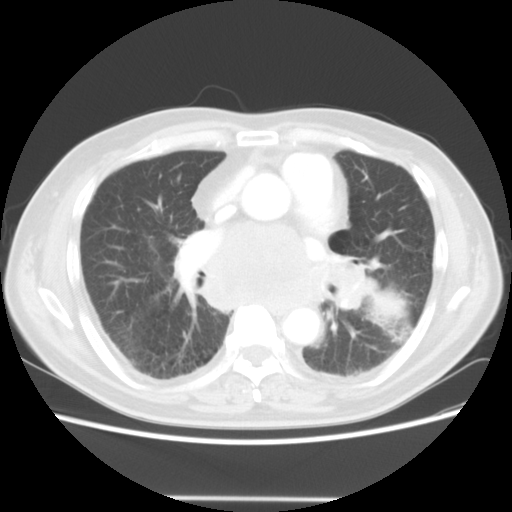
Chest CT, one axial slice. Position 26 of 56 along the scan axis. Reconstruction kernel STANDARD. 140 kVp. Lung window (W 1500 / L -600 HU). 5 mm slice thickness. 512 × 512 image matrix, field of view 360 × 360 mm. Patient: male, 66 years. Case-level facts recorded for this patient, not image findings: clinical TNM (as recorded): T4 N3 M0.
Outlined on this slice (rectangle marked by the reading radiologist):
- lung tumour (recorded histology: small cell carcinoma): bounding box [x1, y1, x2, y2] px = [370, 277, 413, 332]